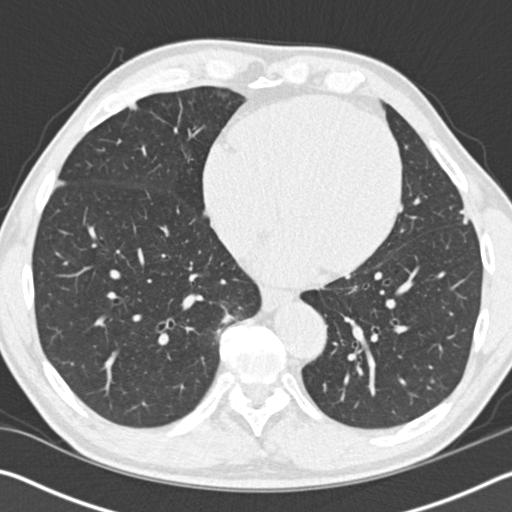
Low-dose screening chest CT, one axial slice; slice 53 of 162 in the series (ordered by position); reconstruction kernel B30f; 120 kVp; lung window (W 1500 / L -600 HU); 2 mm slice thickness; 512 × 512 image matrix, field of view 340 × 340 mm.
Structures marked on this image (outlined manually by an expert reader):
- lesion 1 (tumor, upper lobe of left lung): bounding box (x1, y1, x2, y2) in pixels: (459, 209, 470, 225)